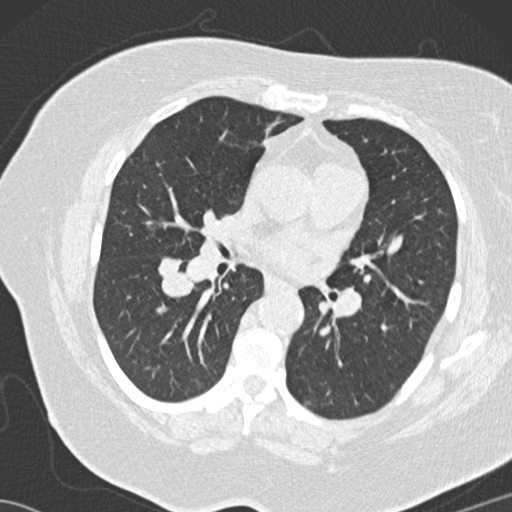
Low-dose screening chest CT, one axial slice. Position 73 of 146 along the scan axis. Reconstruction kernel B30f. Lung window (W 1500 / L -600 HU). 2 mm slice thickness. 512 × 512 image matrix, field of view 350 × 350 mm.
Structures marked on this image (expert manual segmentation):
- lesion 4 (tumor, lower lobe of right lung): bounding box (x1, y1, x2, y2) in pixels: (157, 258, 194, 298)